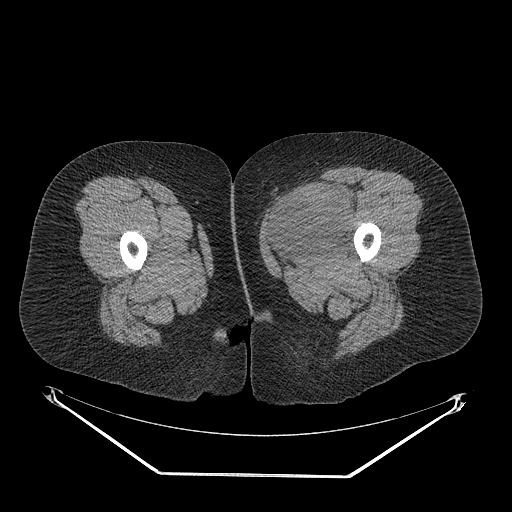
CT of an extremity soft-tissue mass (from a PET/CT study), one axial slice; position 25 of 267 along the scan axis; reconstruction kernel STANDARD; soft-tissue window (W 400 / L 40 HU); 3.75 mm slice thickness; 512 × 512 image matrix, field of view 500 × 500 mm. Female patient. From the clinical record (not read from this slice): histological type: myxofibrosarcoma; grade: intermediate; site of the primary tumour: left thigh.
Outlined on this slice (expert contour drawn on MRI and transferred to this co-registered scan by the dataset authors):
- gross tumour volume including surrounding oedema: bounding box (x1, y1, x2, y2) in pixels: (265, 183, 355, 257)
- gross tumour volume (mass): (269, 189, 353, 255)